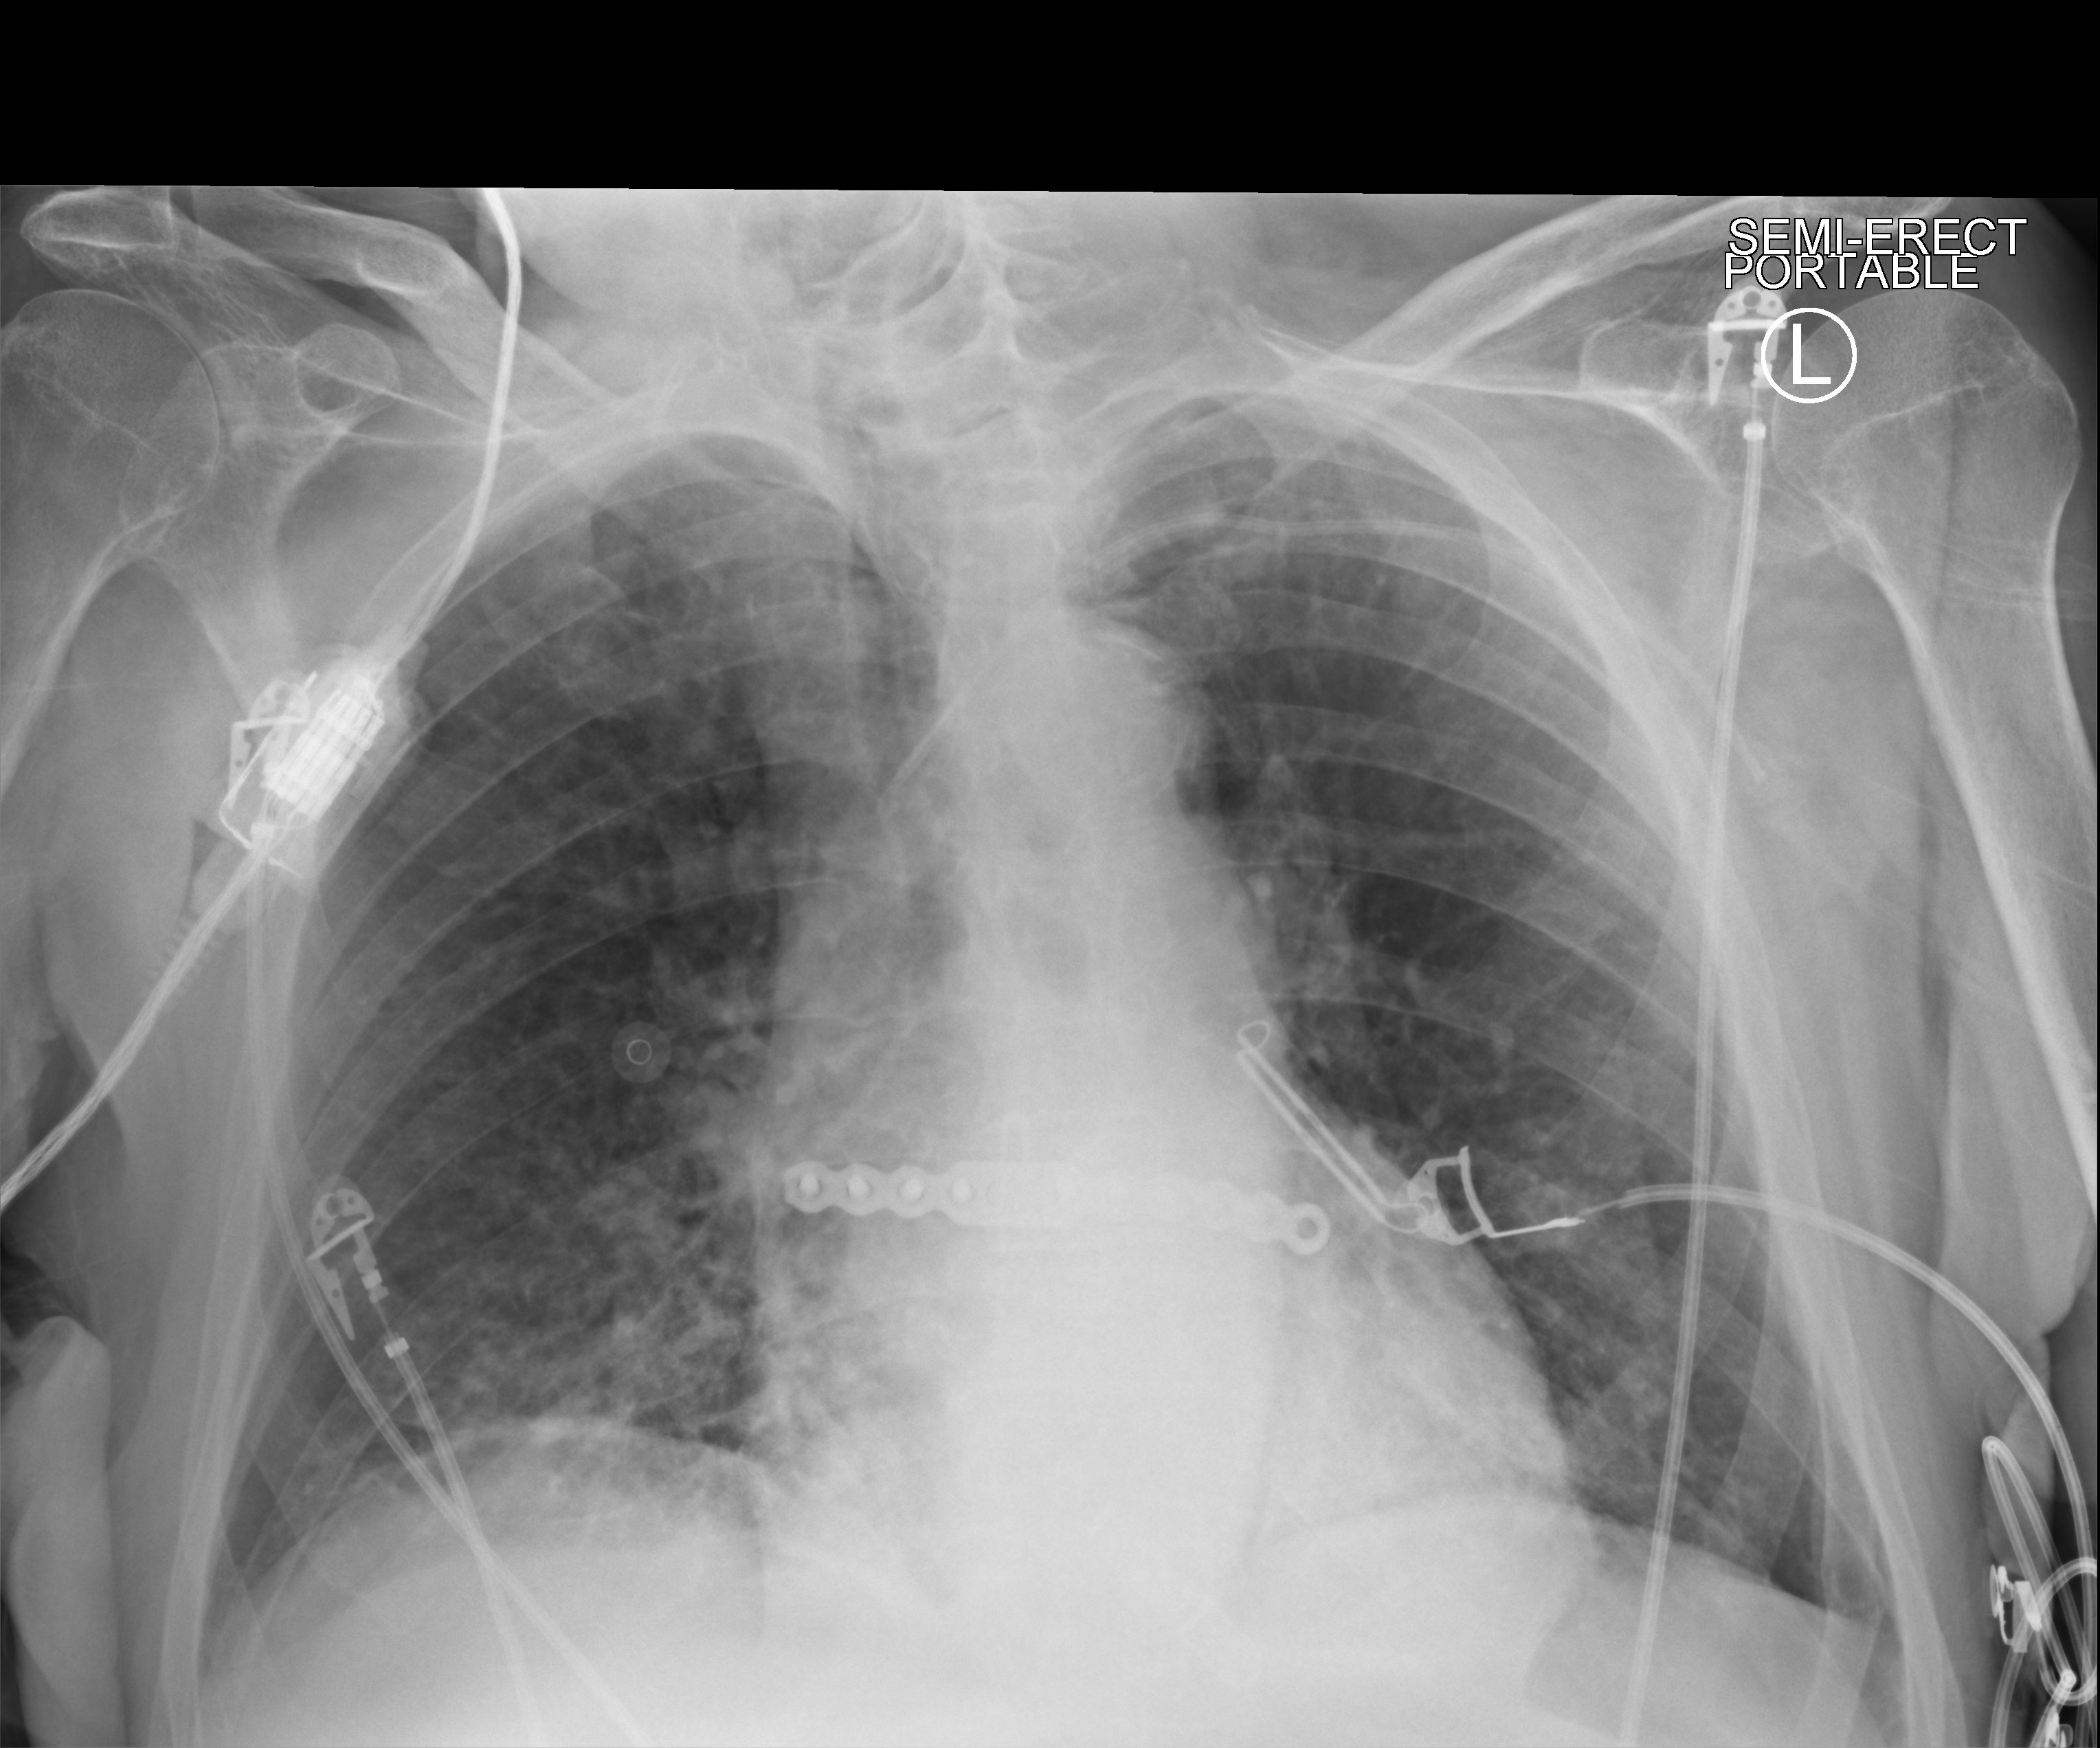
Bedside chest radiograph (computed radiography). Patient hospitalised with COVID-19; male, aged 75–90 years.
From the hospital-stay record, not from the radiograph (when in the stay this image was taken is not recorded):
- COPD (admission record): yes
- mechanically ventilated during this hospital stay: no